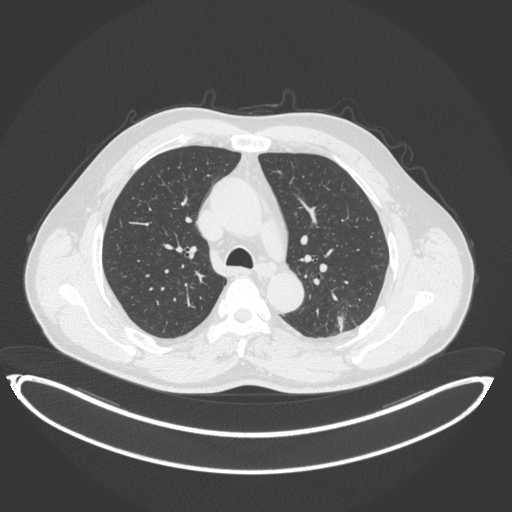
Chest CT, one axial slice. Slice 241 of 399 in the series (ordered by position). 120 kVp. Lung window (W 1500 / L -600 HU). 512 × 512 image matrix, field of view 469 × 469 mm. Patient: male, 58 years. Case-level facts recorded for this patient, not image findings: clinical TNM (as recorded): T1c N0 M0.
Outlined on this slice (rectangle marked by the reading radiologist):
- lung tumour (recorded histology: adenocarcinoma): bounding box (x1, y1, x2, y2) in pixels: (323, 304, 358, 333)